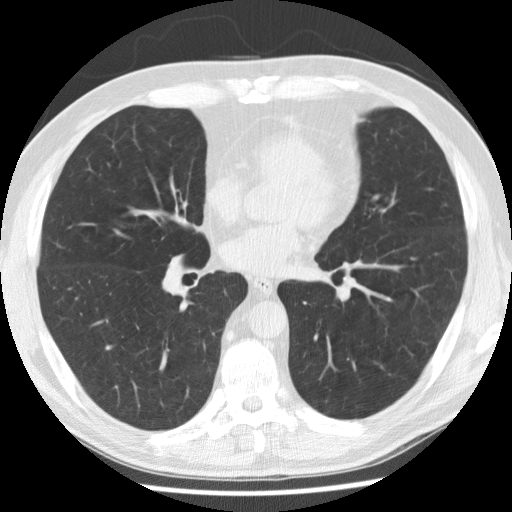
Axial slice from a low-dose chest CT screening exam, baseline screening round, lung window (W 1500 / L -600 HU), 2.5 mm slice thickness, 120 kVp, slice 146 of 265 in the series, 512 × 512 image matrix. Male participant, aged 58 years at enrolment. Former smoker at enrolment.
- Expert-annotated lung lesion, bounding box <368,353,405,387> (left, top, right, bottom; pixels).
- No non-calcified nodule or mass ≥4 mm was recorded by the screening reader at this exam.
- Official screen result: negative screen, no significant abnormalities.
- Lung cancer was diagnosed 798 days after this screen: adenocarcinoma, NOS, left lower lobe, poorly differentiated (G3), stage IA (AJCC 6th edition), 8 mm at pathology.